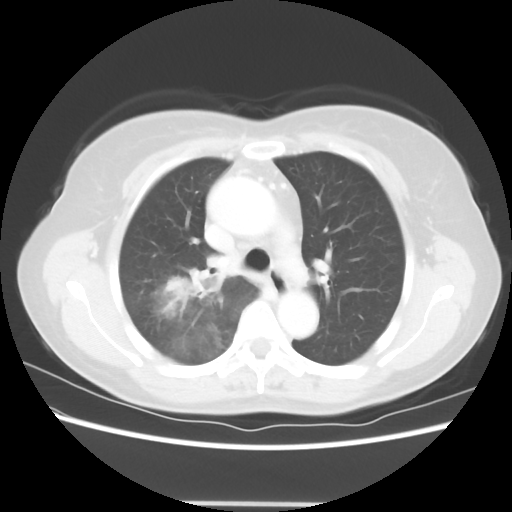
Chest CT, one axial slice; position 40 of 56 along the scan axis; reconstruction kernel STANDARD; lung window (W 1500 / L -600 HU); 5 mm slice thickness; 512 × 512 image matrix. Patient: female, 55 years. Case-level facts recorded for this patient, not image findings: clinical TNM (as recorded): T2 N1 M0; histopathological grade: G2-3.
Annotated regions visible in this slice (bounding box drawn by a radiologist):
- lung tumour (recorded histology: adenocarcinoma): bounding box [x1, y1, x2, y2] px = [144, 253, 227, 333]